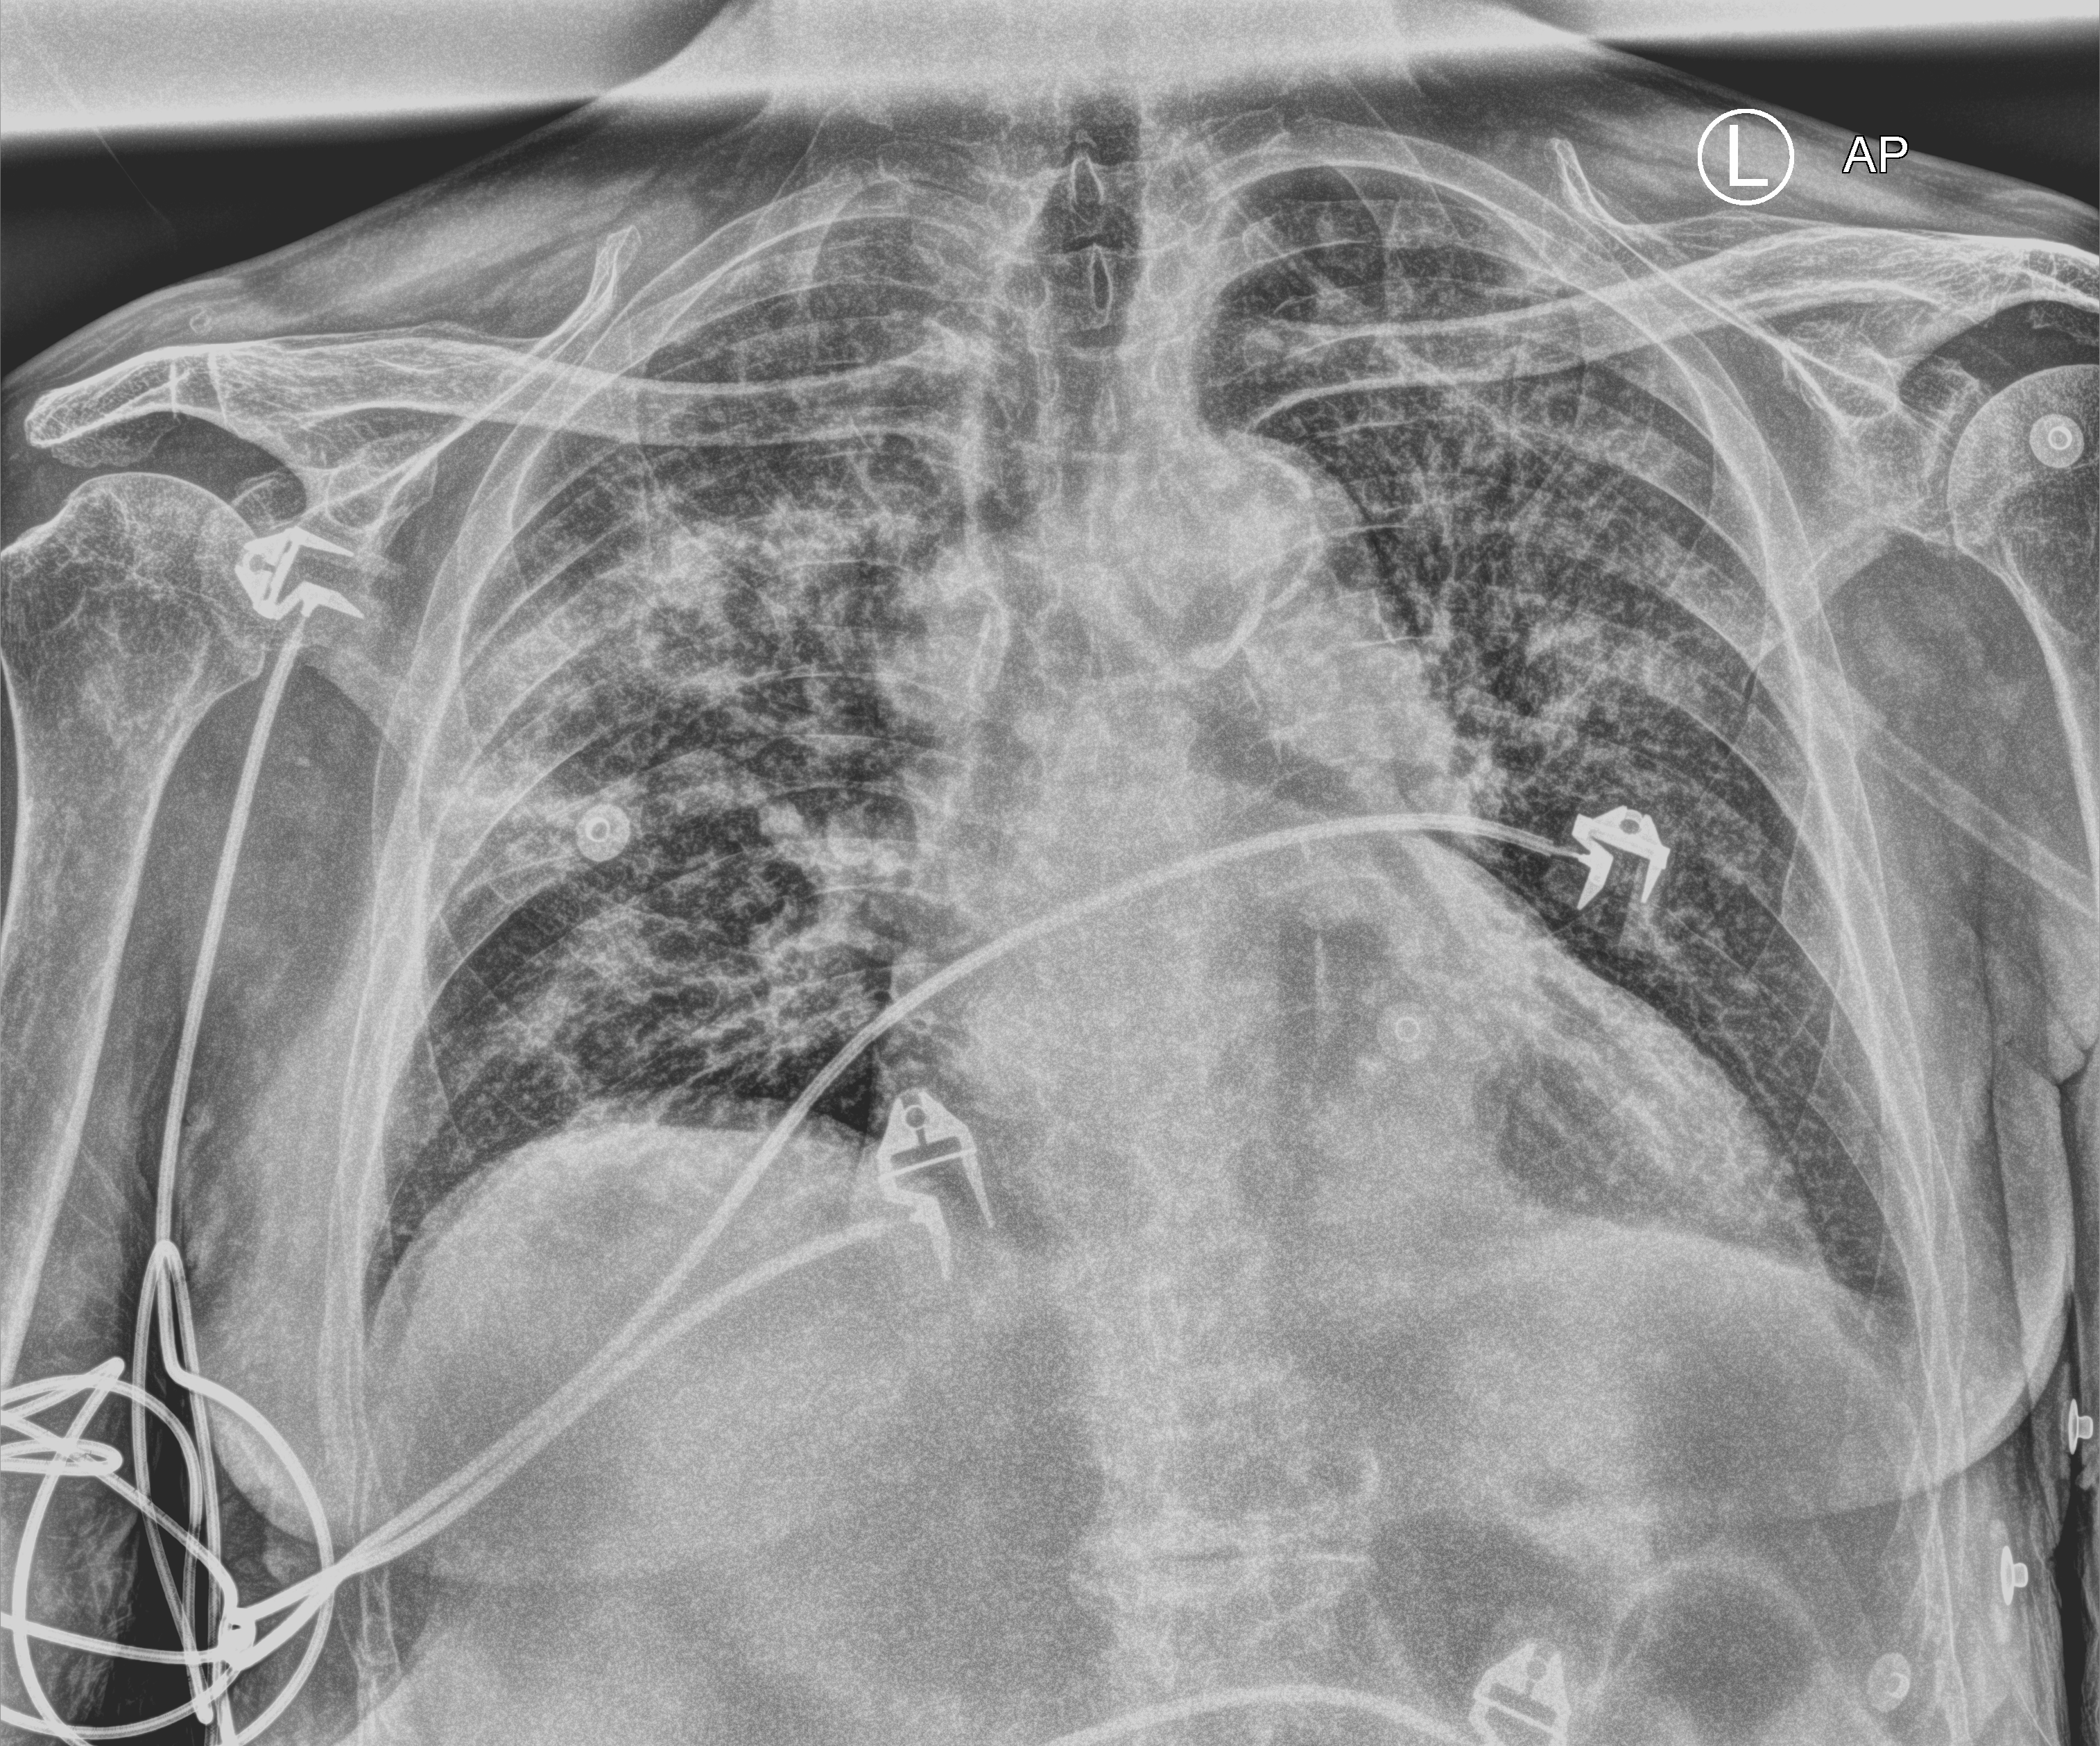
Portable chest radiograph, anteroposterior (AP) projection. Male patient hospitalised with COVID-19, age 75–90 years.
Hospital-stay facts (about this admission, not read from this image; timing relative to this image not recorded): mechanically ventilated during this hospital stay: no; other chronic lung disease (admission record): no.